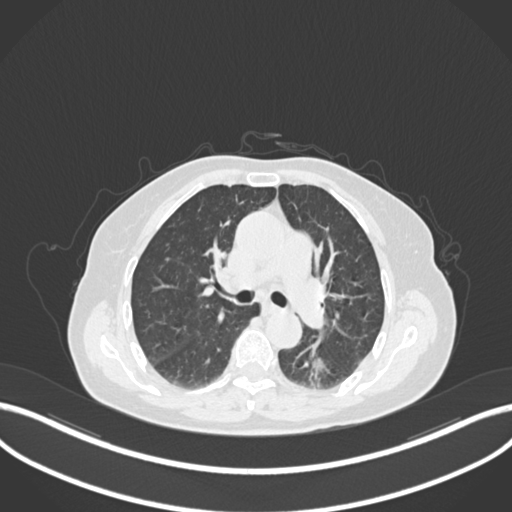
Chest CT, one axial slice; position 529 of 727 along the scan axis; reconstruction kernel B30f; 120 kVp; lung window (W 1500 / L -600 HU); 512 × 512 image matrix. Patient: female, 70 years. Case-level facts recorded for this patient, not image findings: clinical TNM (as recorded): T1c N0 M0.
Annotated regions visible in this slice (bounding box drawn by a radiologist):
- lung tumour (recorded histology: adenocarcinoma): bounding box [x1, y1, x2, y2] px = [305, 340, 336, 385]